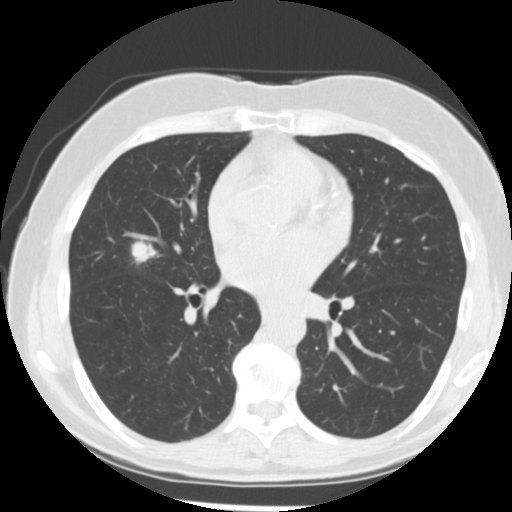
Chest CT (low-dose screening protocol), one axial image. Baseline annual screen. Lung window (W 1500 / L -600 HU). Slice 120 of 255 in the series. 512 × 512 image matrix. Female participant, aged 66 years at enrolment. Former smoker at enrolment.
Expert reader's lesion annotation, bounding box <123,237,162,270> (left, top, right, bottom; pixels). Reader record for this screening exam (exam-level; its link to the box is not recorded): non-calcified nodule or mass ≥4 mm, right middle lobe, 15 × 13 mm, poorly defined margins, soft tissue attenuation. Official screen result: positive, change unspecified: nodule(s) >= 4 mm or enlarging nodule(s), mass(es), or other non-specific abnormalities suspicious for lung cancer. Later outcome: lung cancer diagnosed 27 days after this screen — adenocarcinoma, NOS, right middle lobe, undifferentiated (G4), stage IIIA (AJCC 6th edition), 18 mm at pathology.